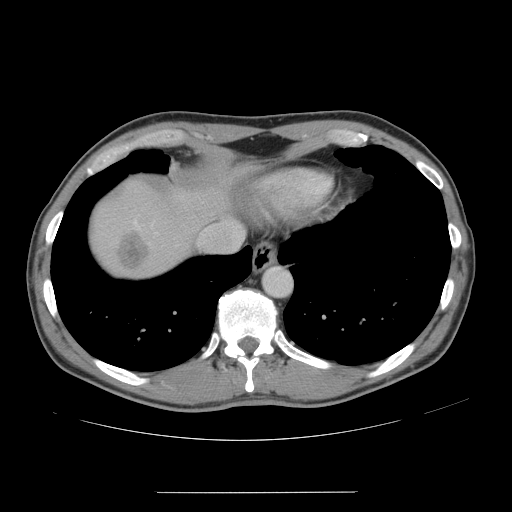
Contrast-enhanced abdominal CT, one axial slice. Slice 137 of 178 in the series (ordered by position). Intravenous contrast given. Soft-tissue window (W 400 / L 40 HU). 512 × 512 image matrix, field of view 401 × 401 mm. Male patient, age 53 years. Case-level facts recorded for this patient, not image findings: diagnosis: colorectal cancer liver metastases, imaged before liver resection; multiple liver metastases: yes; largest metastasis: 2.4 cm.
Outlined on this slice (expert manual segmentation):
- liver: bounding box [x1, y1, x2, y2] px = [90, 182, 231, 277]
- planned liver remnant (the part of the liver to remain after resection): [189, 184, 232, 216]
- liver metastasis: [117, 232, 147, 267]